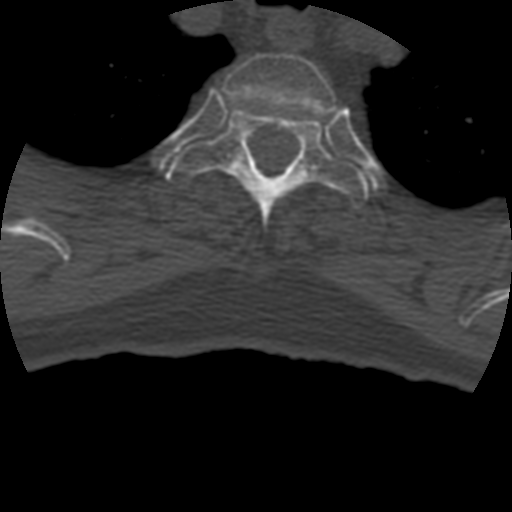
CT including the spine, one axial slice; slice 357 of 399 in the series (ordered by position); reconstruction kernel STANDARD; 120 kVp; bone window (W 1800 / L 400 HU); 1.25 mm slice thickness; 512 × 512 image matrix, field of view 160 × 160 mm. Patient age 69 years. From the clinical record (not read from this slice): primary cancer: prostate.
Annotated regions visible in this slice (semi-automatic segmentation, software-assisted and operator-edited):
- T2 vertebra: bounding box [x1, y1, x2, y2] px = [222, 53, 337, 120]
- T3 vertebra: [165, 107, 368, 230]